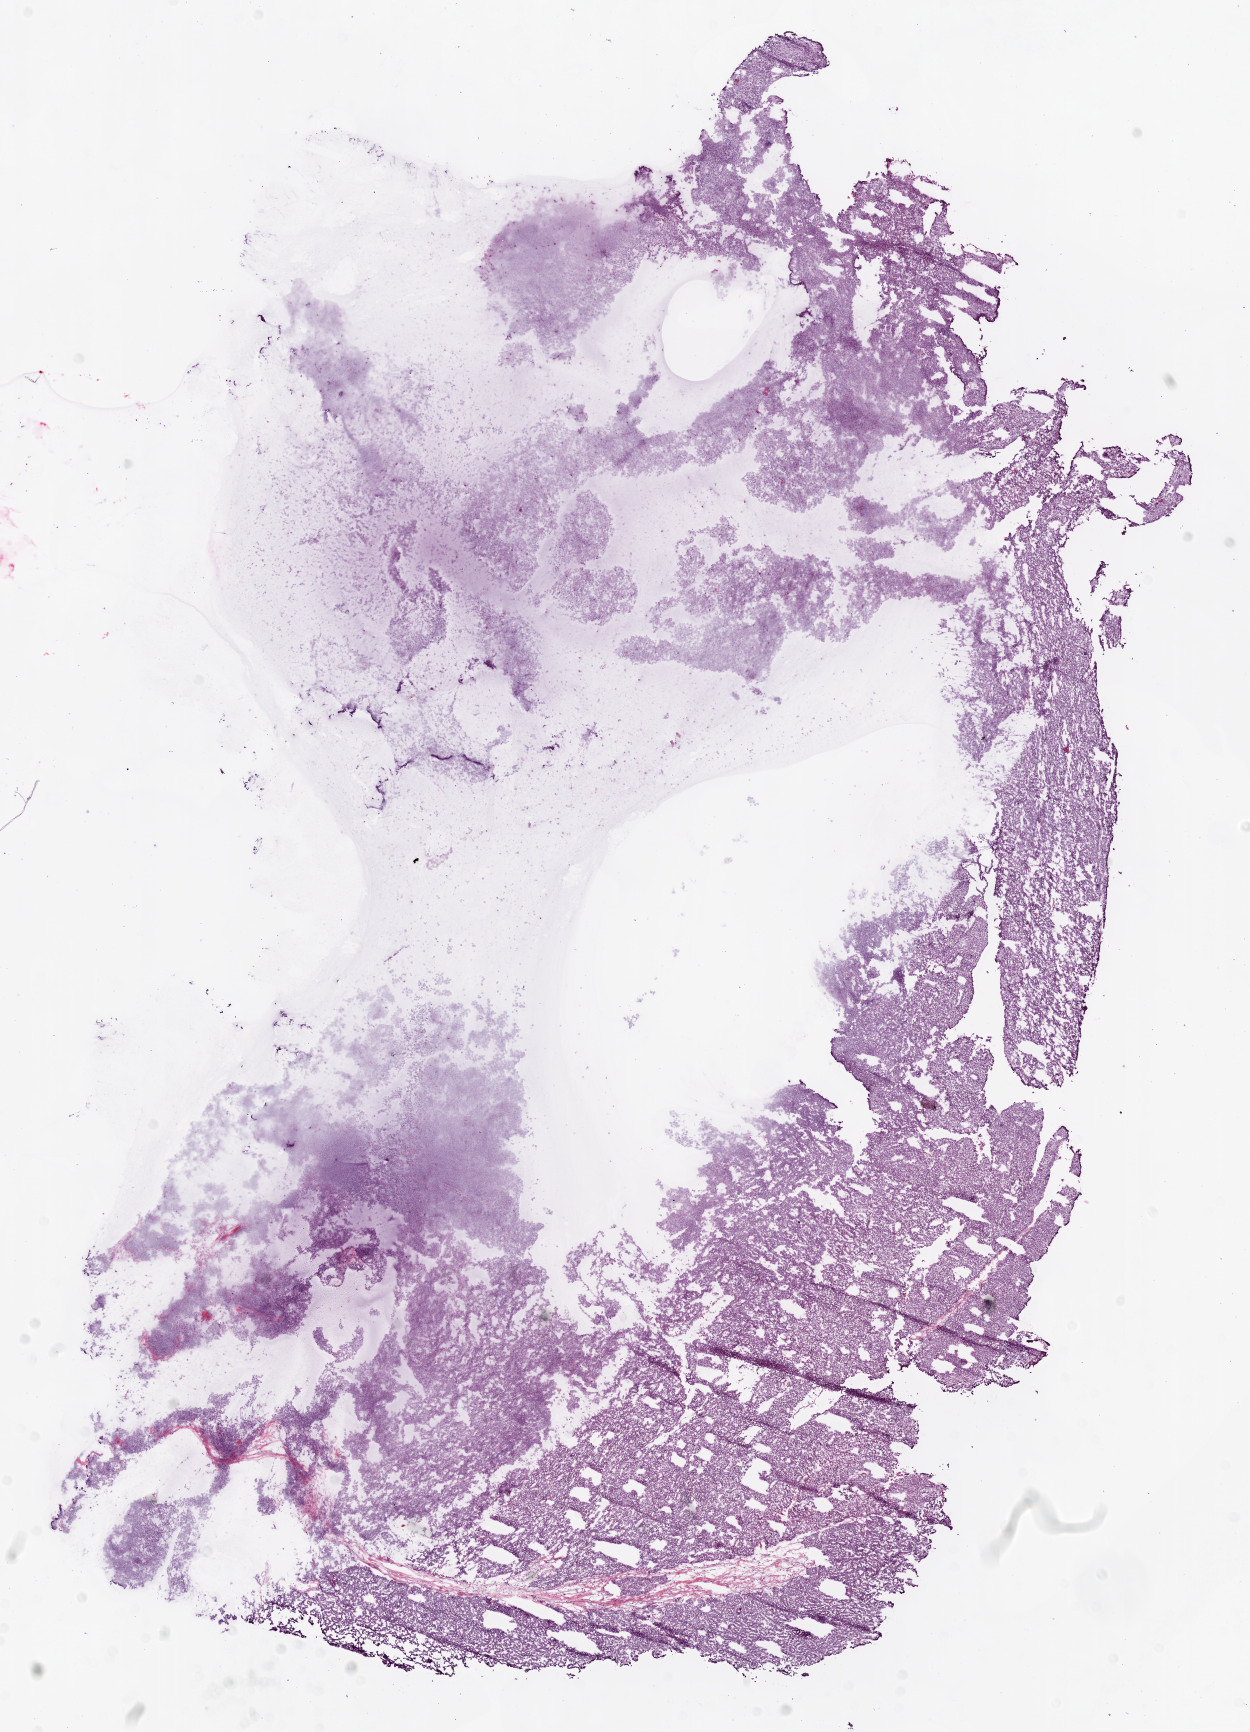
H&E-stained whole-slide image, shown as a low-resolution overview of the whole scanned area (about 10.0 x 13.9 mm). Frozen section from the bottom of the tissue portion. Primary tumour sample from the ovary. Female, age 62 years at initial diagnosis. Histologic grade: G3 (poorly differentiated). Slide review estimates, as recorded: tumour cells 98%, tumour nuclei 95%, normal cells 0%, stromal cells 0%, necrosis 2%.
Laterality: bilateral. Histologic diagnosis: Serous cystadenocarcinoma, NOS. FIGO stage: IIIC.